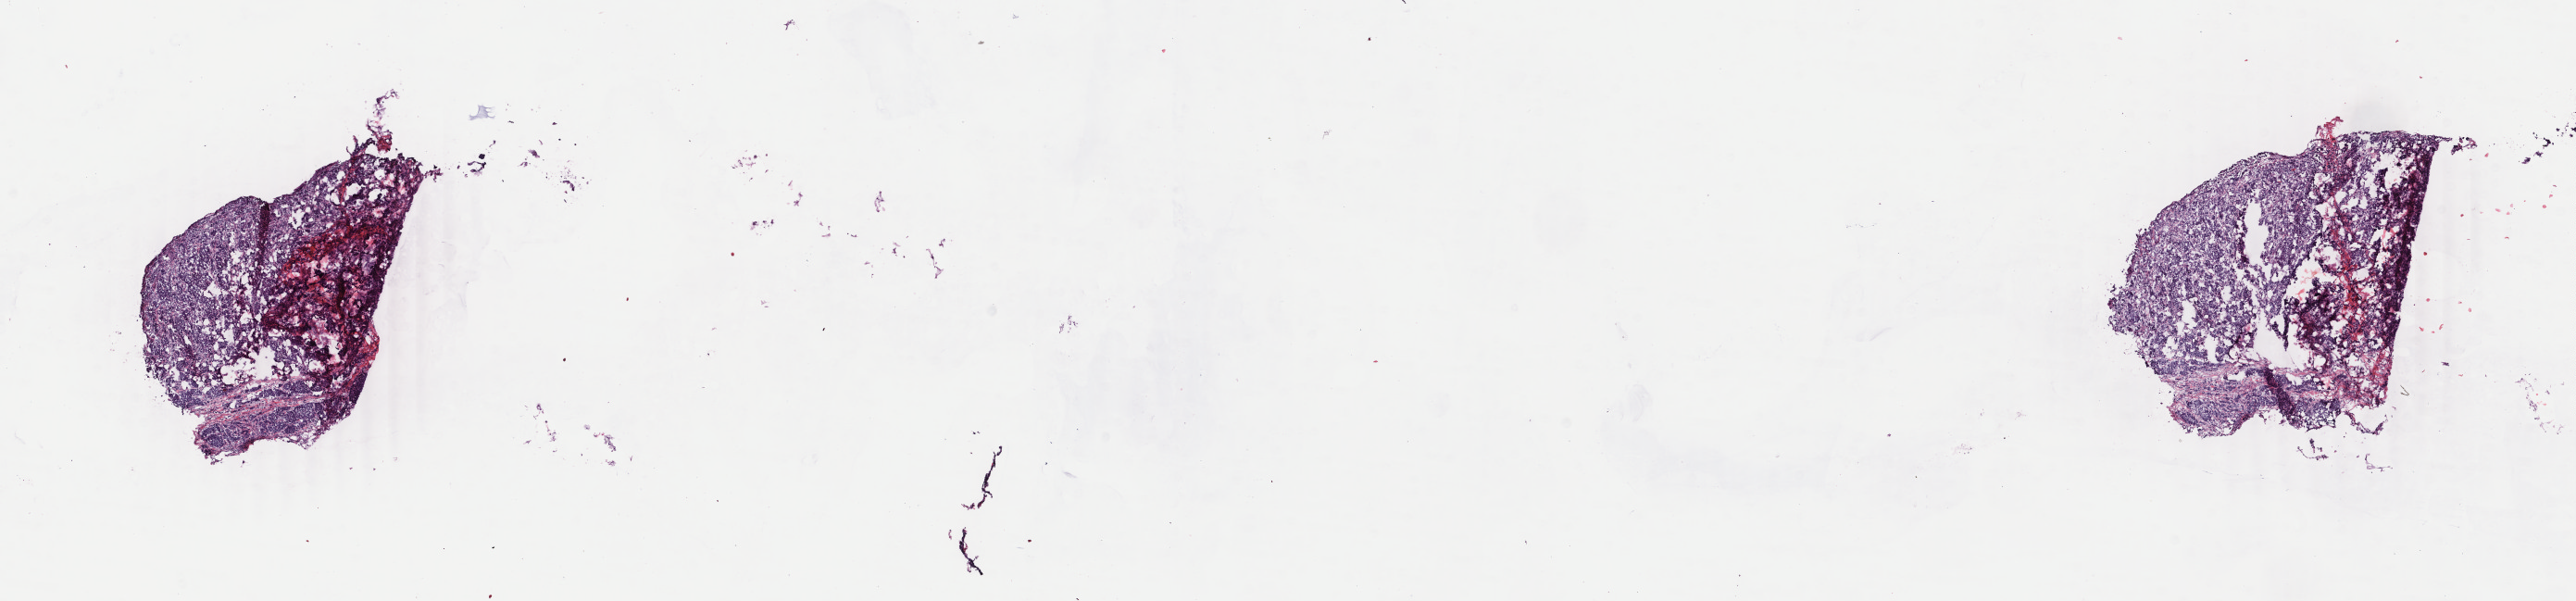
Digitized H&E tissue section (whole slide), low-resolution overview of the scanned area, about 22.1 x 5.2 mm. Frozen section from the bottom of the tissue portion. Breast, primary tumour sample. Patient: female, age at initial diagnosis 63 years. Pathologist review of this section (percent, as recorded): tumour cells 88%, tumour nuclei 95%, normal cells 0%, stromal cells 12%, necrosis 0%. Infiltration values recorded for this section: lymphocyte infiltration 1%, monocyte infiltration 0%, neutrophil infiltration 0%.
AJCC pathologic stage: IV (6th edition). TNM: T2 N2a M1. Lymph nodes positive (case pathology): 8 of 9 examined. Histologic diagnosis: Infiltrating duct carcinoma, NOS.